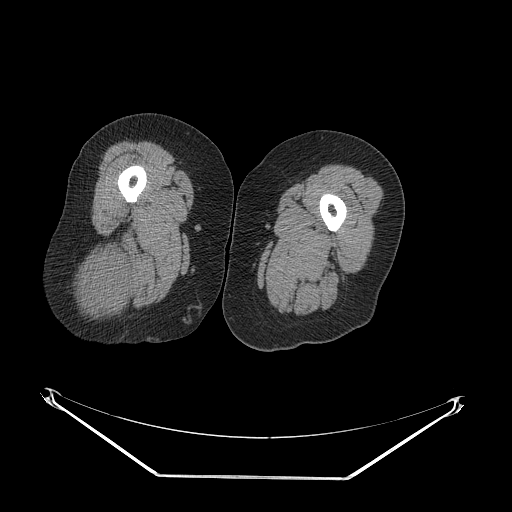
CT of an extremity soft-tissue mass (from a PET/CT study), one axial slice; slice 29 of 257 in the series (ordered by position); soft-tissue window (W 400 / L 40 HU); 3.75 mm slice thickness; 512 × 512 image matrix, field of view 500 × 500 mm. Female patient. Case-level facts recorded for this patient, not image findings: histological type: synovial sarcoma; grade: intermediate; site of the primary tumour: right buttock.
Outlined on this slice (expert contour drawn on MRI and transferred to this co-registered scan by the dataset authors):
- gross tumour volume including surrounding oedema: bounding box [x1, y1, x2, y2] px = [78, 242, 131, 312]
- gross tumour volume (mass): [80, 251, 131, 307]